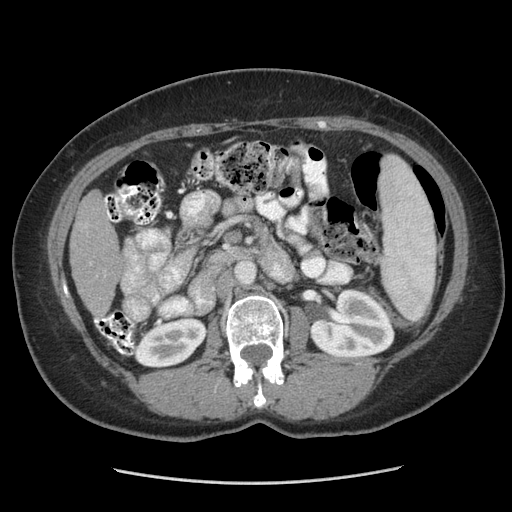
Contrast-enhanced abdominal CT (liver protocol), one axial slice. 140 kVp. Soft-tissue window (W 400 / L 40 HU). 2.5 mm slice thickness. 512 × 512 image matrix, field of view 360 × 360 mm. Case-level facts recorded for this patient, not image findings: diagnosis: hepatocellular carcinoma (patient treated with transarterial chemoembolisation; whether this scan precedes or follows treatment is not stated here); TNM stage (as recorded): Stage-I; Child-Pugh class: A; tumour differentiation: poorly differentiated.
Outlined on this slice (semi-automatic segmentation, software-assisted and operator-edited):
- liver parenchyma outside the tumour (the mass and vessels are separate outlines, so this box may not span the whole liver): bounding box <70,190,120,316> (left, top, right, bottom; pixels)
- liver vessels: <106,201,110,217>